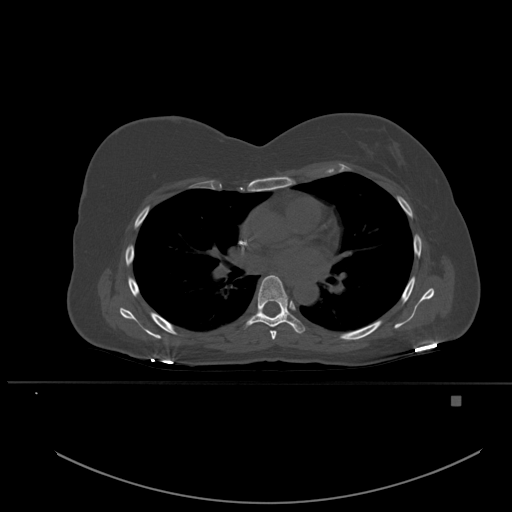
CT including the spine, one axial slice. Position 352 of 651 along the scan axis. Bone window (W 1800 / L 400 HU). 1.5 mm slice thickness. 512 × 512 image matrix. Female patient, age 49 years. From the clinical record (not read from this slice): primary cancer: breast.
Annotated regions visible in this slice (semi-automatic segmentation, software-assisted and operator-edited):
- T5 vertebra: bounding box (x1, y1, x2, y2) in pixels: (270, 330, 277, 340)
- T6 vertebra: (247, 275, 305, 334)